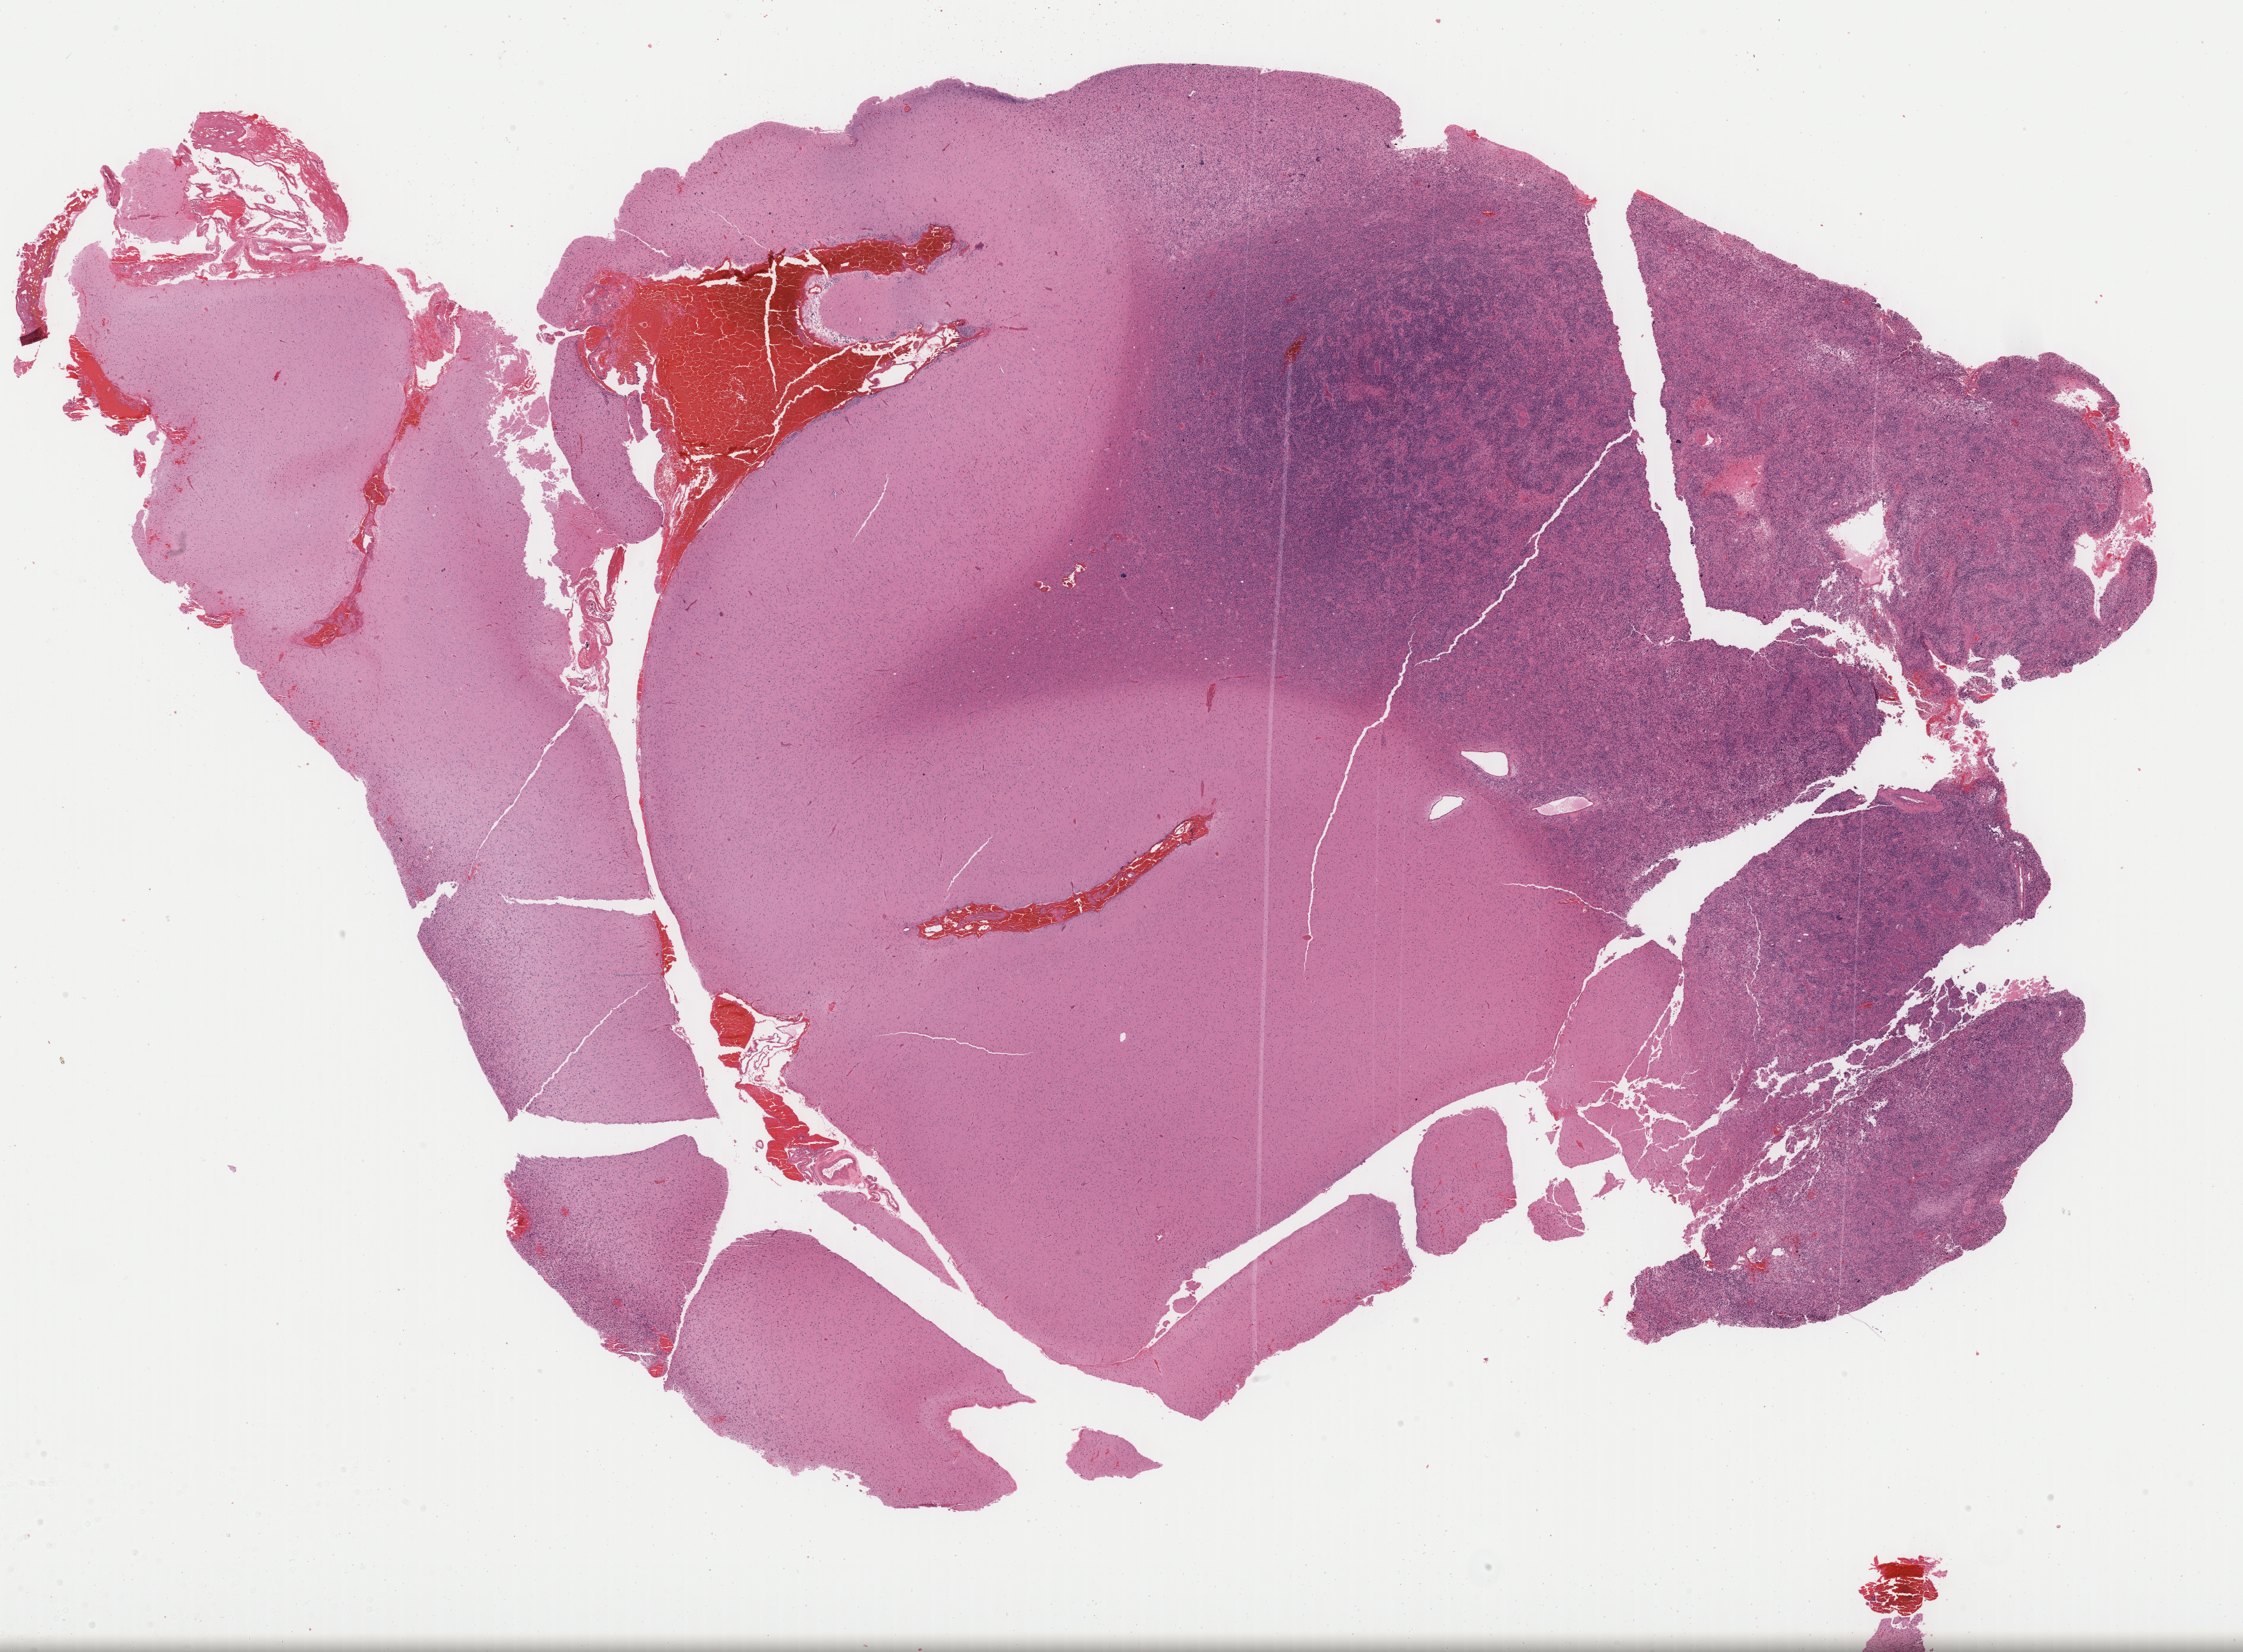
Whole-slide histology image, H&E, low-resolution overview of the scanned area, about 27.7 x 20.4 mm; formalin-fixed paraffin-embedded (FFPE) diagnostic section; brain, primary tumour sample. Male, age 65 years at initial diagnosis.
- diagnosis: Glioblastoma